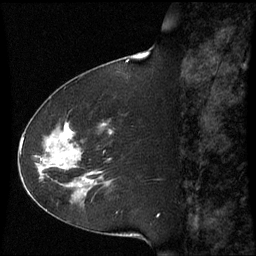
Breast MRI (dynamic contrast-enhanced), one sagittal slice; slice 23 of 60 in the series (ordered by position); dynamic contrast-enhanced series, image 2 of 3 at this slice position (ordered by acquisition); 1.5 T; TE 4.2 ms, TR 8.9 ms; 2.3 mm slice thickness; 256 × 256 image matrix, field of view 210 × 210 mm. Patient: female, 51 years. Case-level facts recorded for this patient, not image findings: setting: breast cancer imaged before/during neoadjuvant chemotherapy; receptor status: HR-positive, HER2-negative.
Annotated regions visible in this slice (semi-automatically segmented with operator editing):
- analysis volume of interest (the breast-tissue region the enhancement analysis was run in; not a lesion): box from (x=50, y=123) to (x=114, y=187) px
- tumour enhancement mask (voxels above the 70 % enhancement threshold inside the analysis volume of interest): (x=50, y=125)–(x=88, y=181)